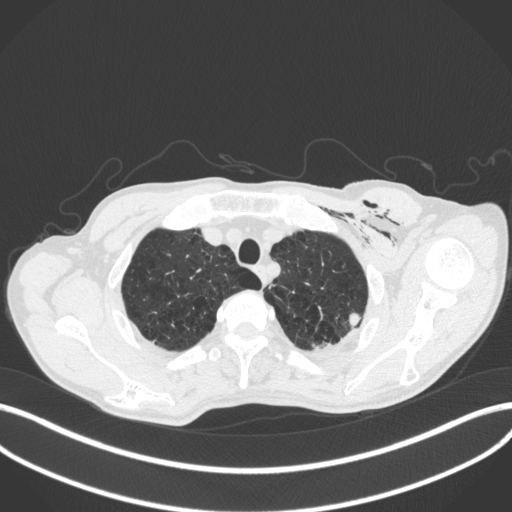
Chest CT, one axial slice. Position 358 of 416 along the scan axis. 120 kVp. Lung window (W 1500 / L -600 HU). 512 × 512 image matrix. Patient: male, 58 years. From the clinical record (not read from this slice): clinical TNM (as recorded): T3 N0 M0.
Annotated regions visible in this slice (bounding box drawn by a radiologist):
- lung tumour (recorded histology: adenocarcinoma): bounding box <346,309,364,328> (left, top, right, bottom; pixels)